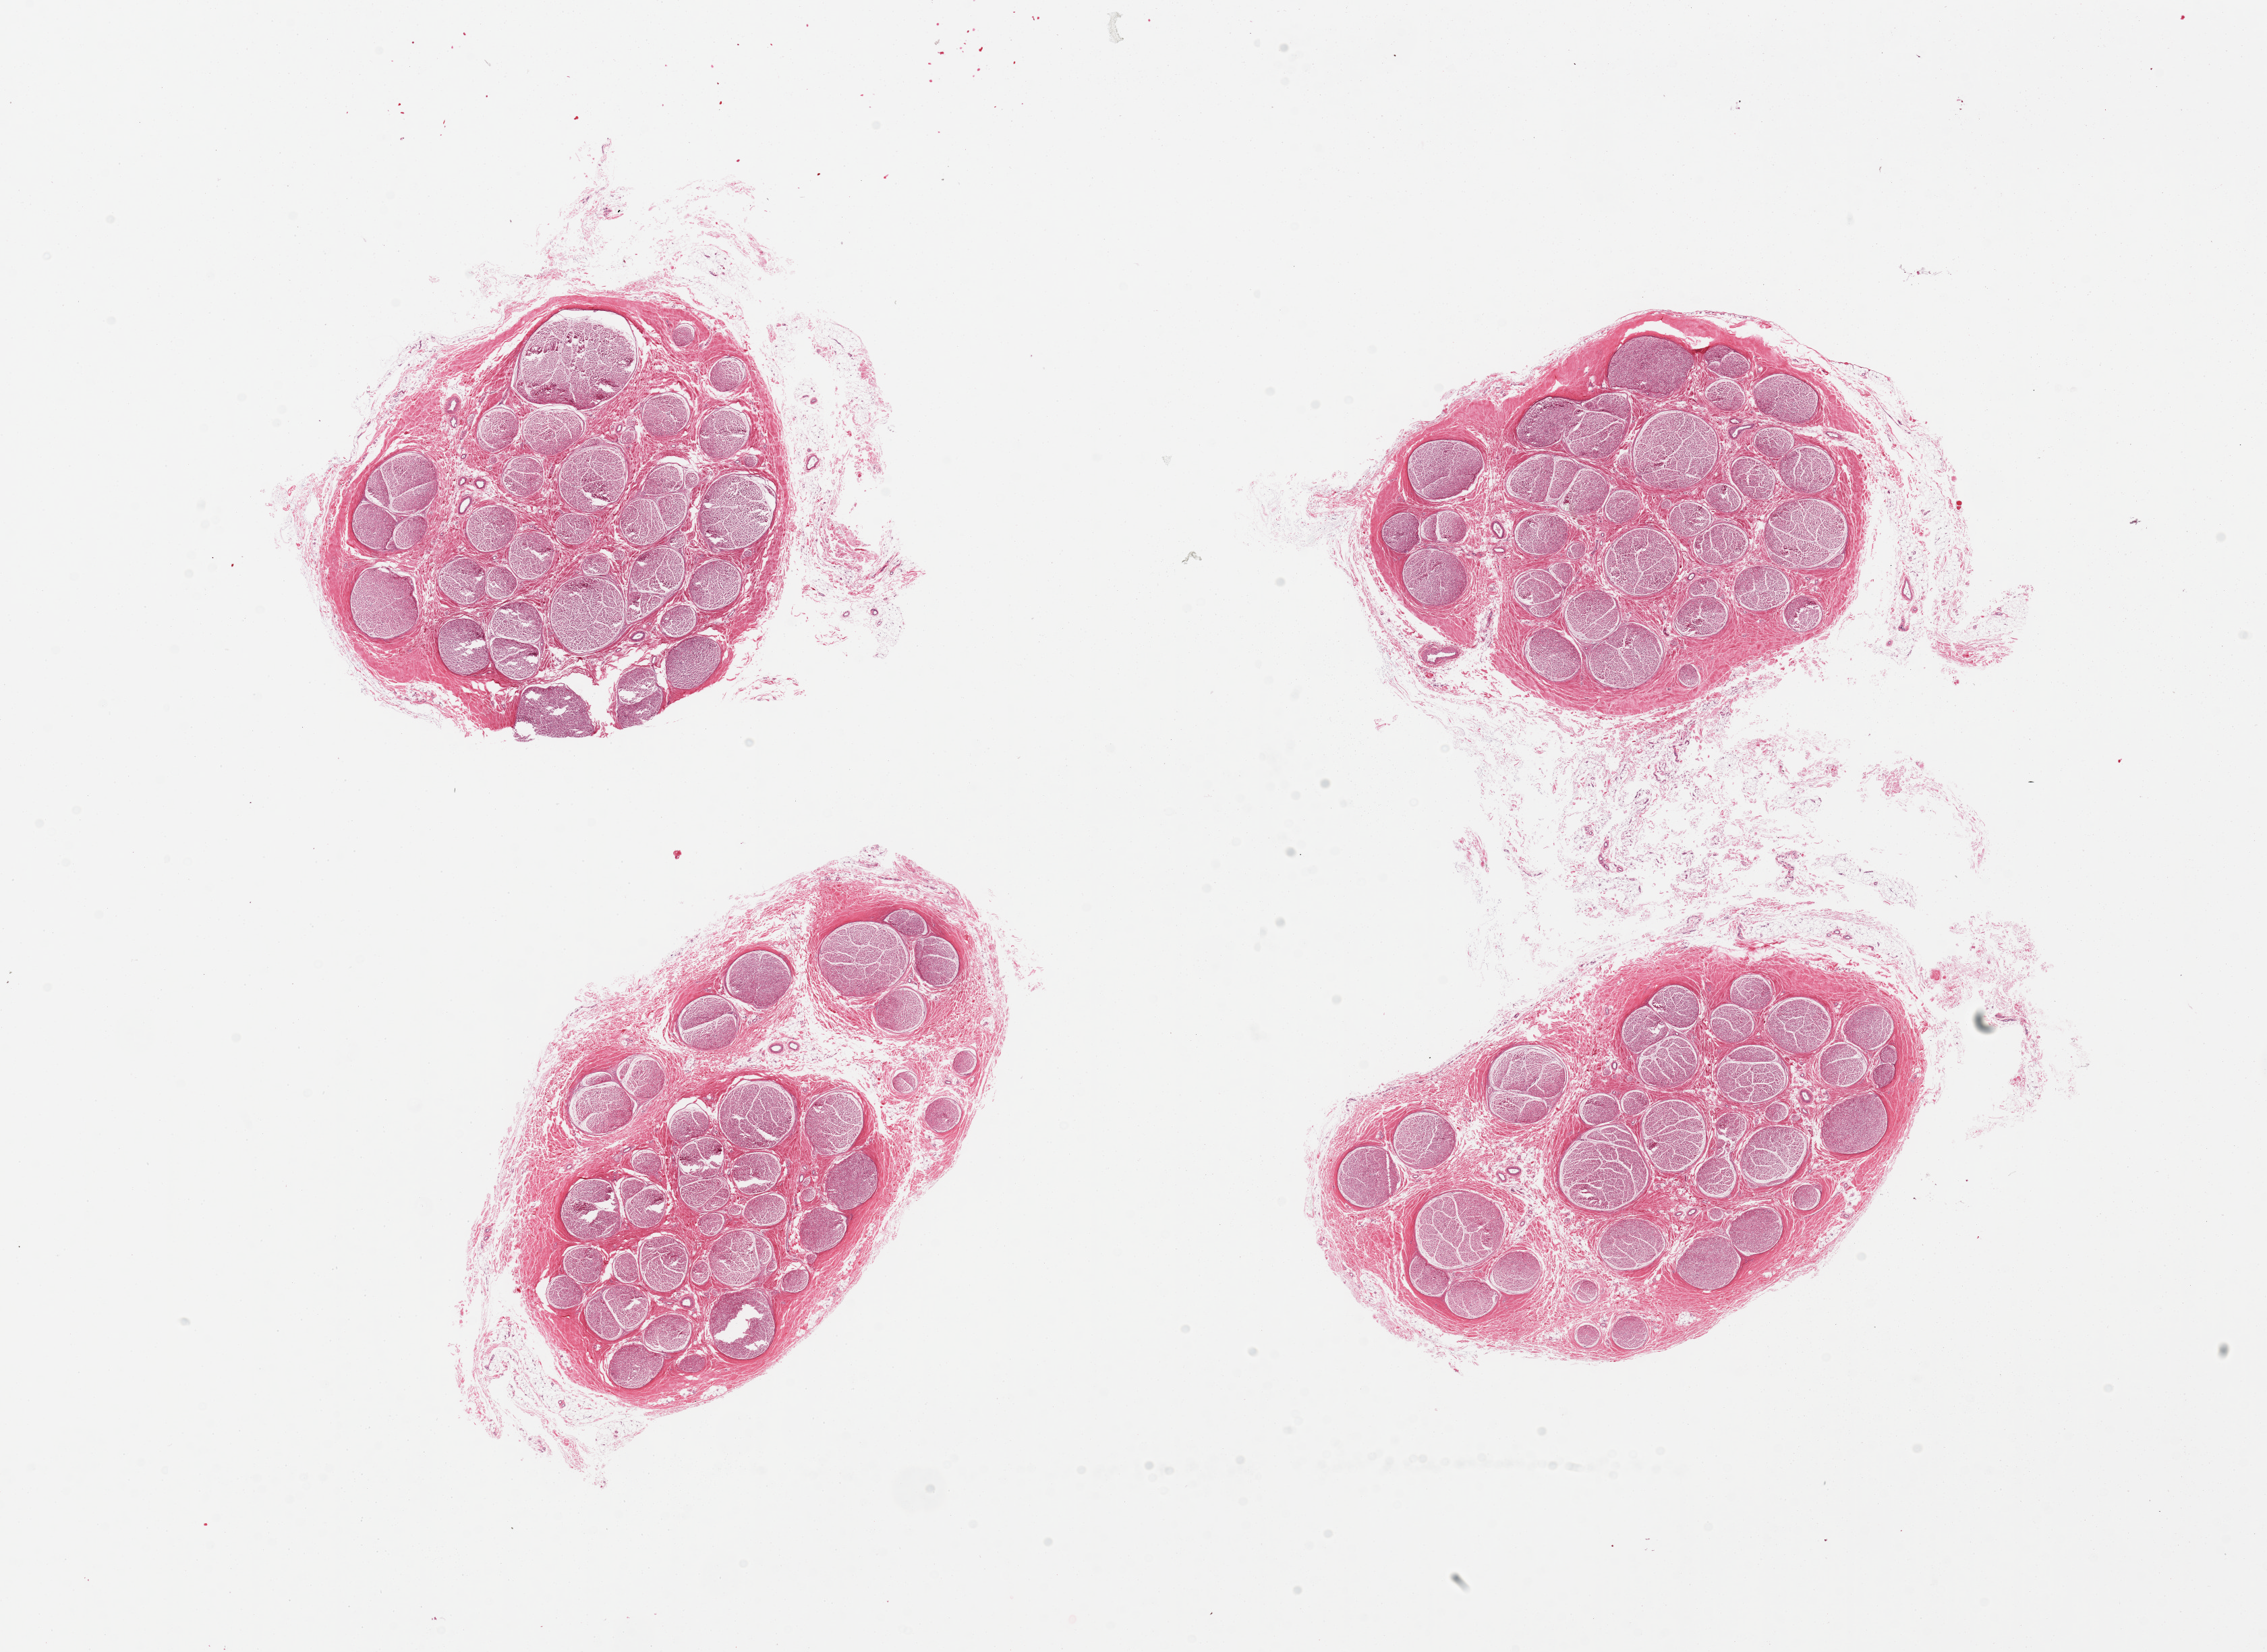
Whole-slide image, haematoxylin and eosin stain, low-resolution overview of the scanned area, about 26.6 x 19.4 mm (slide scanned at 20x). PAXgene-fixed paraffin-embedded (PFPE) section. Section of tibial nerve (target tissue). Donor tissue sample.
Review note (as recorded): 4 pieces, loose perineural stroma.